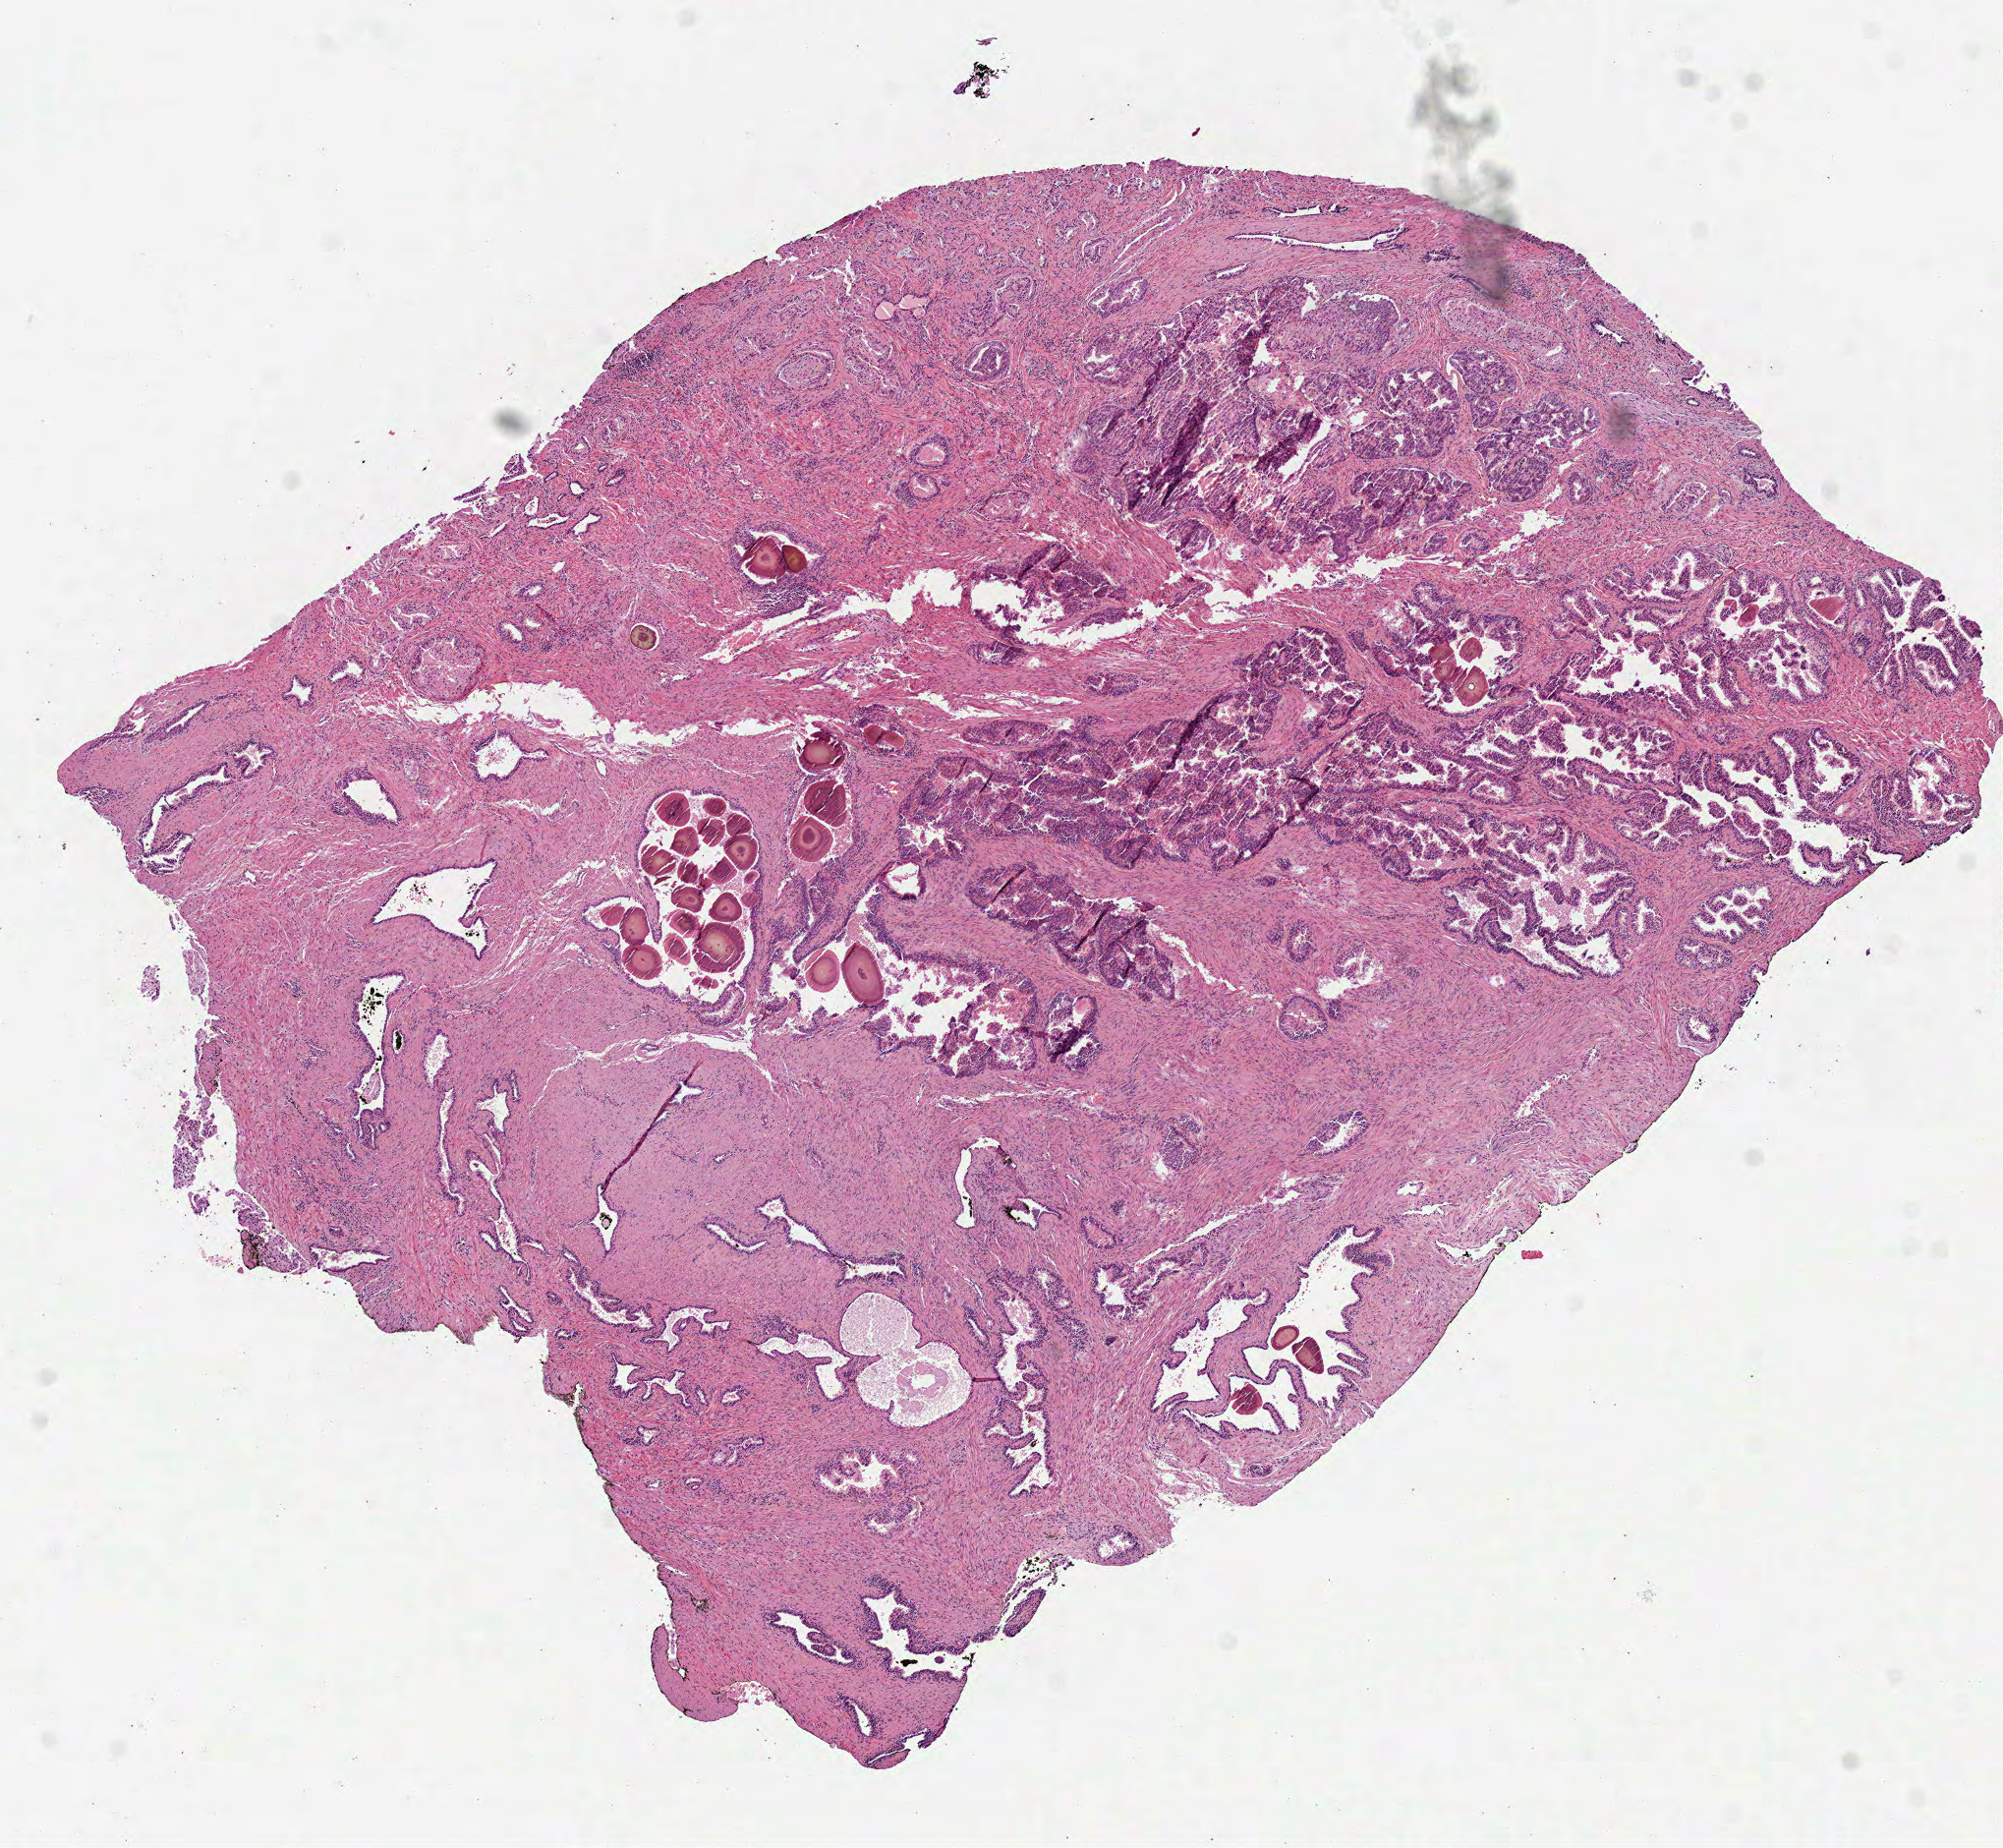
Hematoxylin and eosin (H&E) stained whole-slide image — whole scanned area (about 8.2 x 7.6 mm, slide scanned at 40x) shown as a low-resolution overview, formalin-fixed paraffin-embedded (FFPE) diagnostic section, primary tumour sample from the prostate. Male patient; age at initial diagnosis 62 years. Gleason score: 9 (4+5).
Histologic diagnosis: Acinar cell carcinoma (prostate gland). Laterality: bilateral.